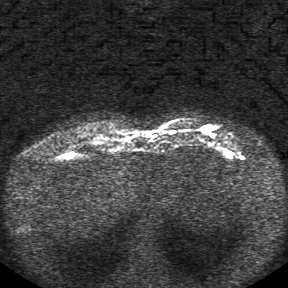
Breast MRI, one axial slice; diffusion-weighted series; image 2 of 4 stored at this slice position (different b-values; order by instance number); 1.5 T; 5 mm slice thickness; 288 × 288 image matrix, field of view 340 × 340 mm. Female patient.
Annotated regions visible in this slice (manually delineated by an expert):
- tumour on diffusion-weighted imaging: bounding box (x1, y1, x2, y2) in pixels: (207, 124, 212, 128)